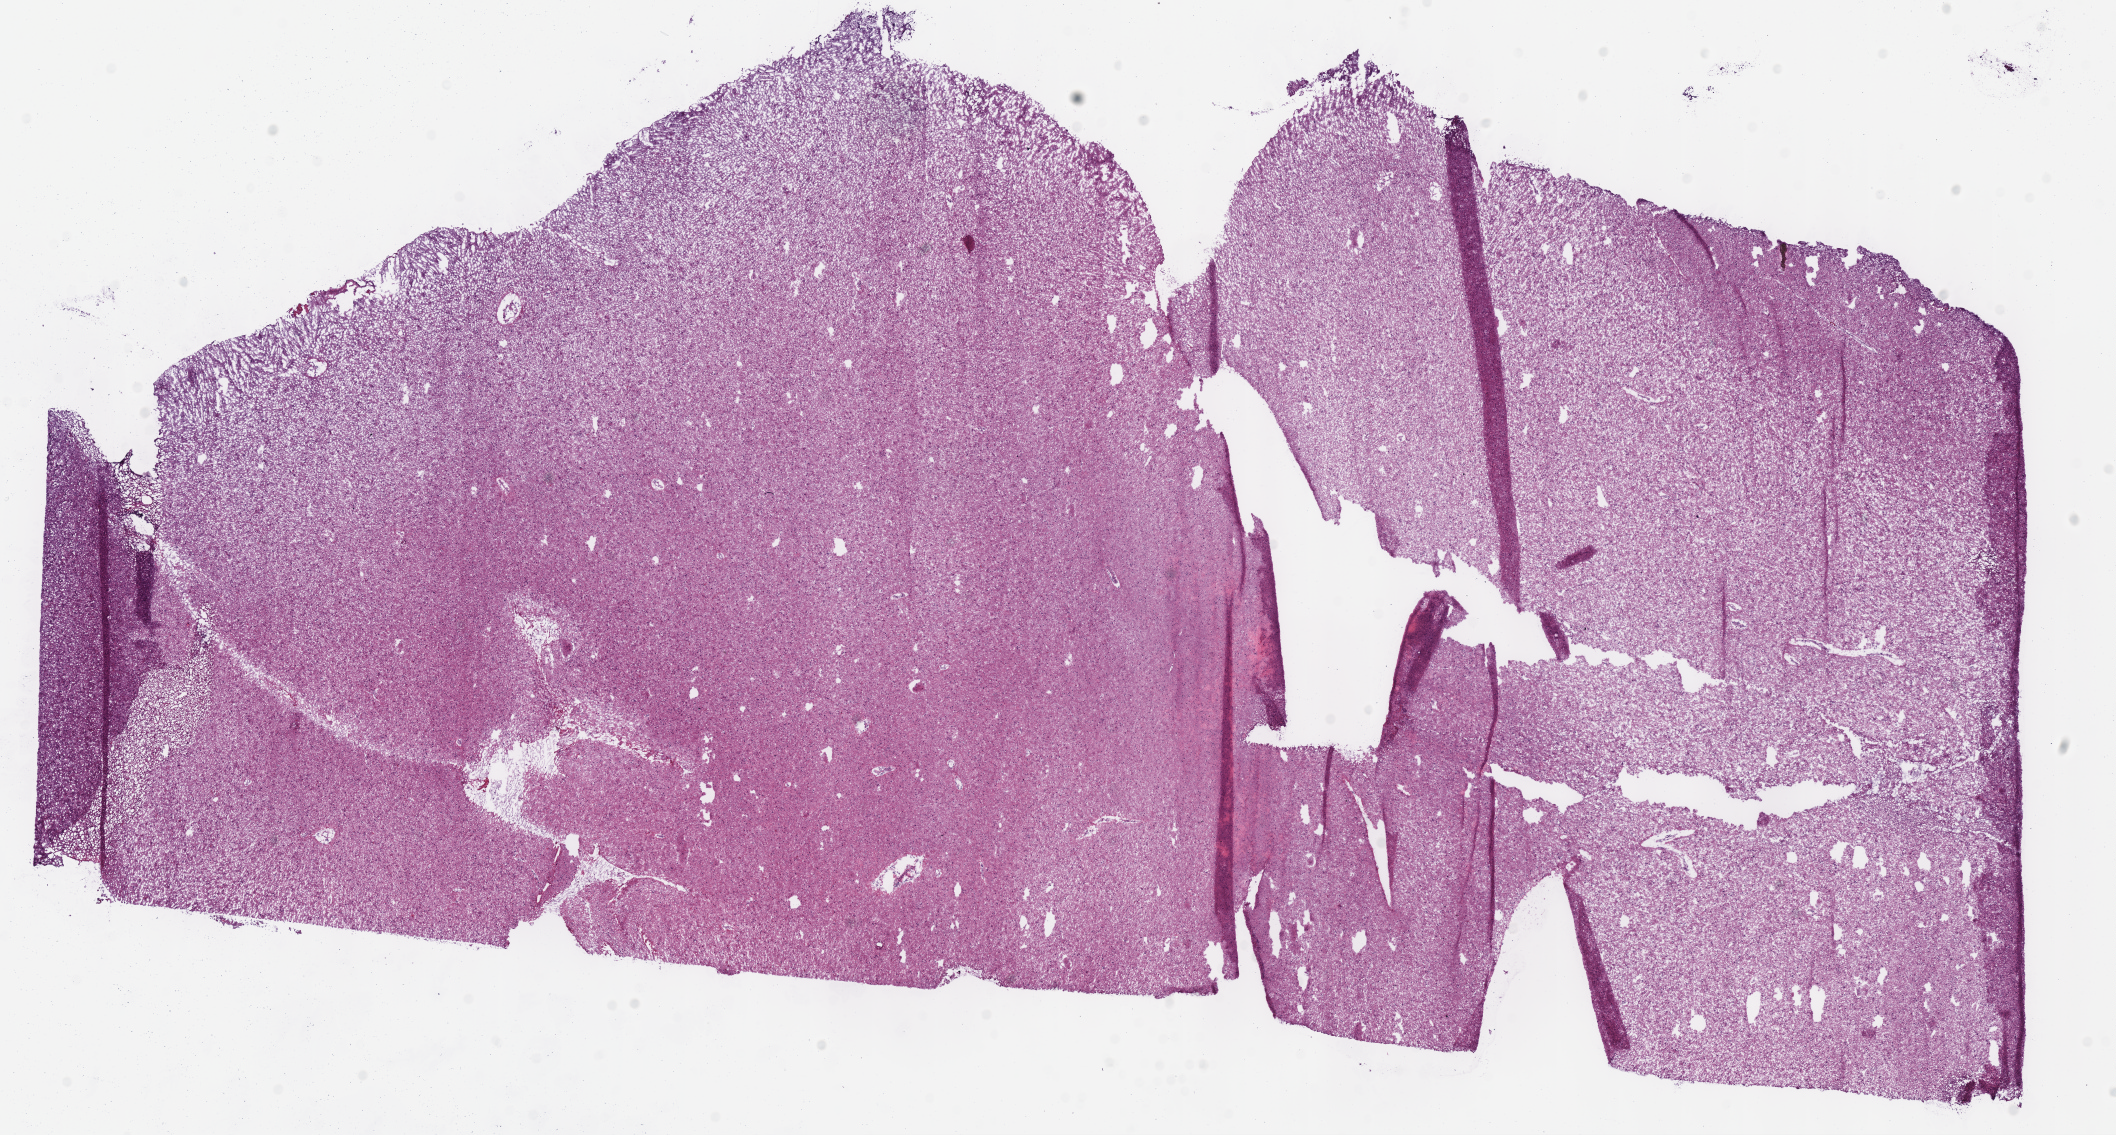
H&E whole-slide image, a low-resolution overview of the entire scanned area, about 16.6 x 8.9 mm (slide scanned at 40x), frozen section from the bottom of the tissue portion, sample: primary tumour, brain. Male patient; age at initial diagnosis 32 years. Histologic grade: G3 (poorly differentiated). Slide review estimates, as recorded: tumour cells 100%, tumour nuclei 70%, normal cells 0%, stromal cells 0%, necrosis 0%.
- pathologic diagnosis: Mixed glioma (cerebrum)